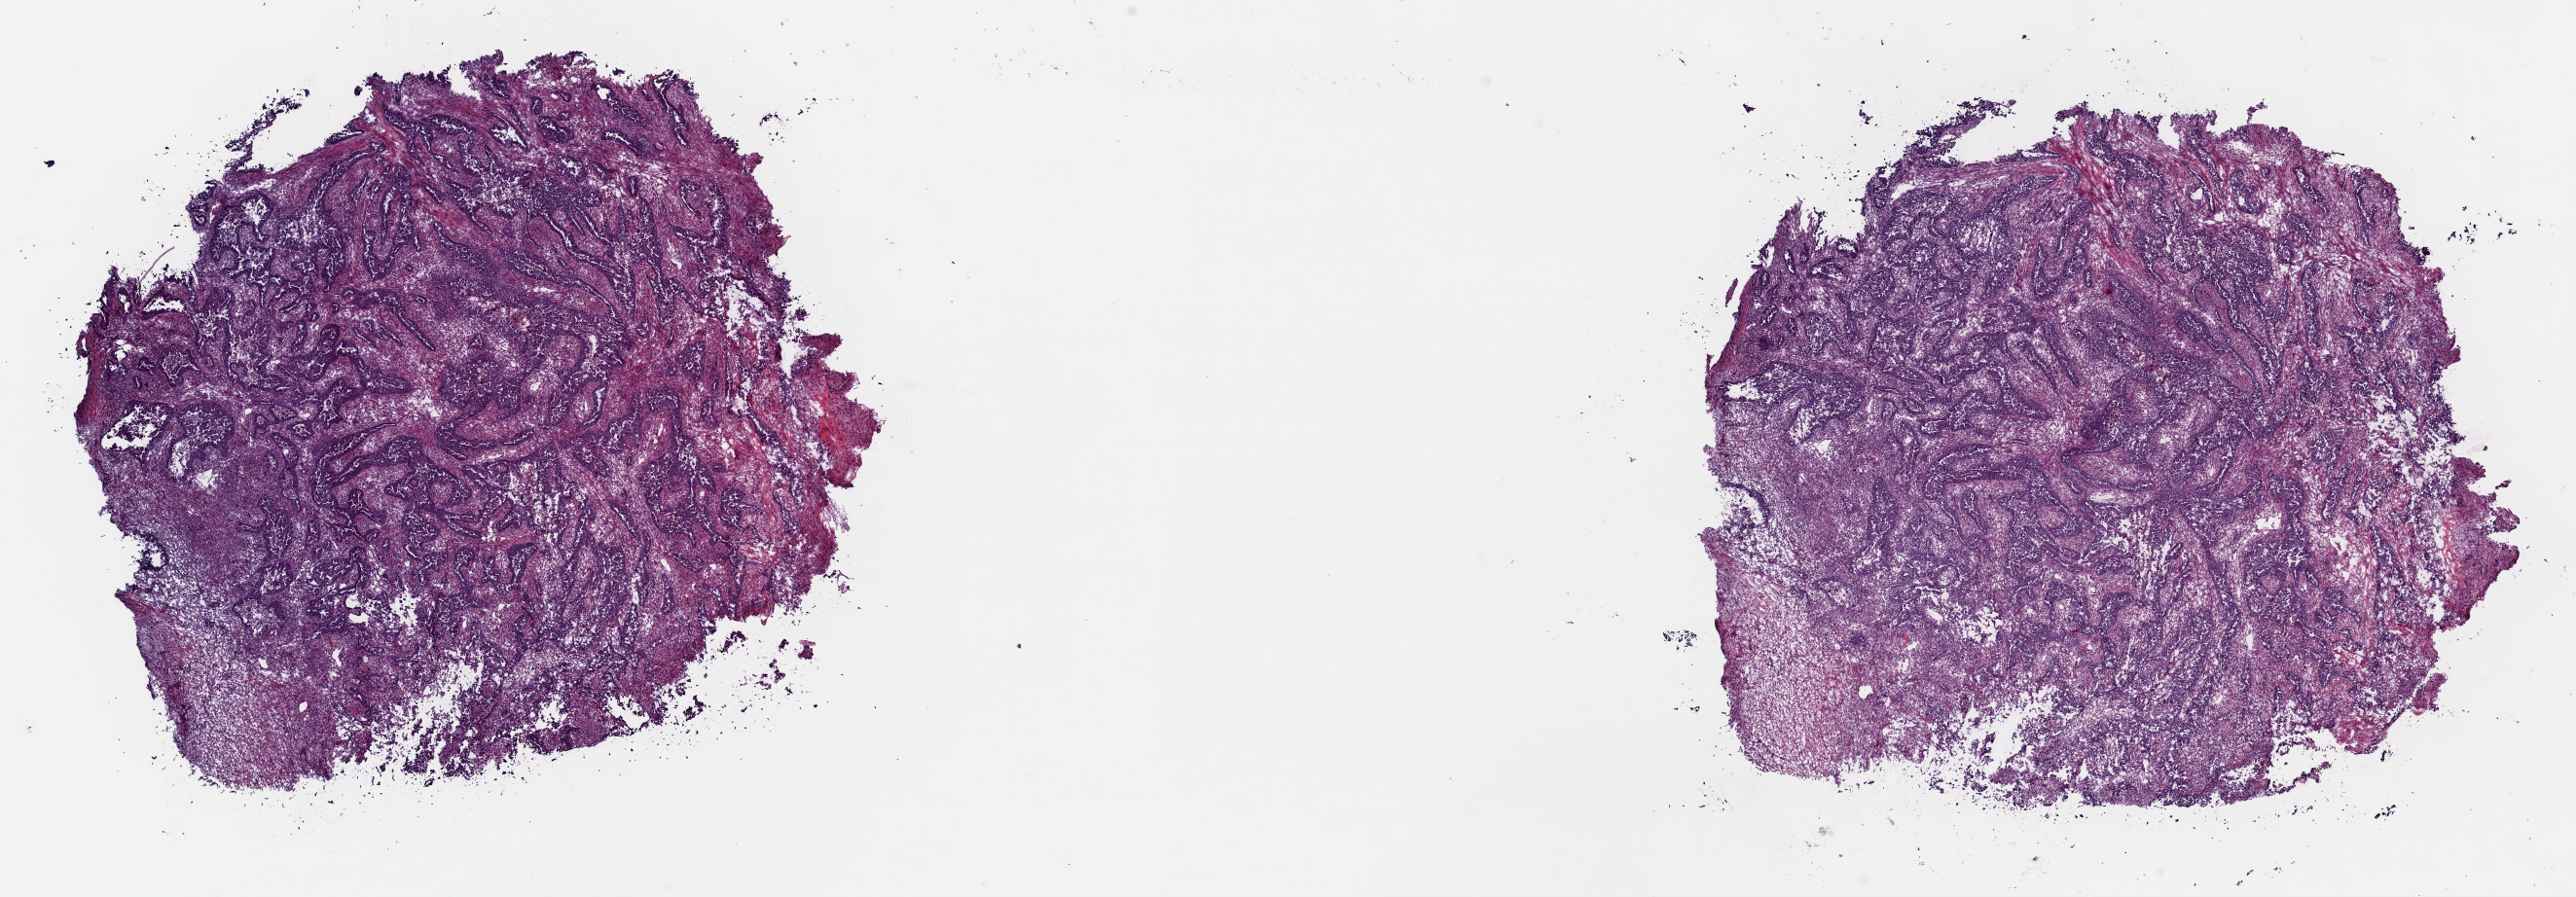
Whole-slide histology image, H&E — low-resolution overview of the scanned area, about 20.9 x 7.3 mm; frozen section; sample: primary tumour, uterus. Patient: female, age at initial diagnosis 70 years. Histologic grade: G3 (poorly differentiated). Slide review estimates, as recorded: tumour cells 95%, tumour nuclei 65%, normal cells 0%, stromal cells 0%, necrosis 5%. Infiltration values recorded for this section: lymphocyte infiltration 5%, monocyte infiltration 1%, neutrophil infiltration 1%.
* FIGO stage: IIIA
* pathologic diagnosis: Serous cystadenocarcinoma, NOS (endometrium)